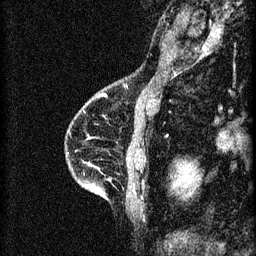
Breast MRI (dynamic contrast-enhanced), one sagittal slice. Position 20 of 60 along the scan axis. 3 images stored at this slice position (order not interpretable as contrast timing). 1.5 T. TE 4.2 ms, TR 8.2 ms. 256 × 256 image matrix. Female patient, age 46 years.
Outlined on this slice (semi-automatically segmented with operator editing):
- analysis volume of interest (the breast-tissue region the enhancement analysis was run in; not a lesion): bounding box (x1, y1, x2, y2) in pixels: (65, 114, 148, 209)
- tumour enhancement mask (voxels above the 70 % enhancement threshold inside the analysis volume of interest): (89, 184, 92, 187)